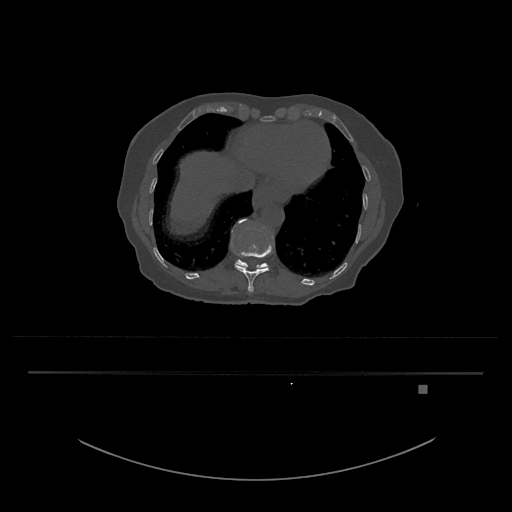
CT including the spine, one axial slice. Position 648 of 797 along the scan axis. Reconstruction kernel Br40s/3. 120 kVp. Bone window (W 1800 / L 400 HU). 512 × 512 image matrix, field of view 500 × 500 mm. Patient: female, 57 years. From the clinical record (not read from this slice): primary cancer: cervical.
Annotated regions visible in this slice (semi-automatically segmented with operator editing):
- T11 vertebra: box from (x=231, y=219) to (x=271, y=292) px
- T12 vertebra: (x=235, y=219)–(x=269, y=270)